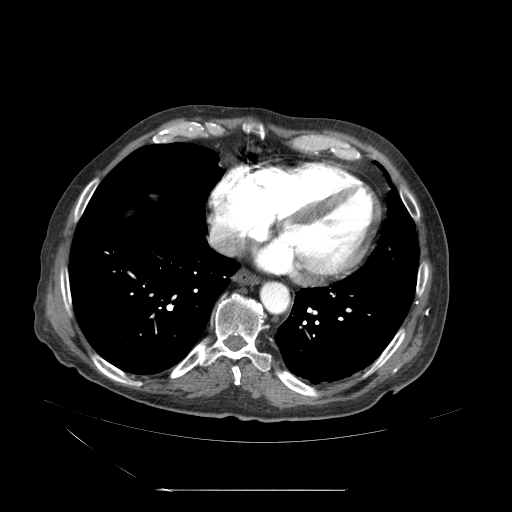
Contrast-enhanced abdominal CT (liver protocol), one axial slice. Position 63 of 71 along the scan axis. 120 kVp. Soft-tissue window (W 400 / L 40 HU). 512 × 512 image matrix, field of view 440 × 440 mm. From the clinical record (not read from this slice): diagnosis: hepatocellular carcinoma (patient treated with transarterial chemoembolisation; whether this scan precedes or follows treatment is not stated here); TNM stage (as recorded): Stage-II; Child-Pugh class: A; tumour size: 1 cm.
Outlined on this slice (semi-automatically segmented with operator editing):
- abdominal aorta: bounding box [x1, y1, x2, y2] px = [260, 280, 289, 315]